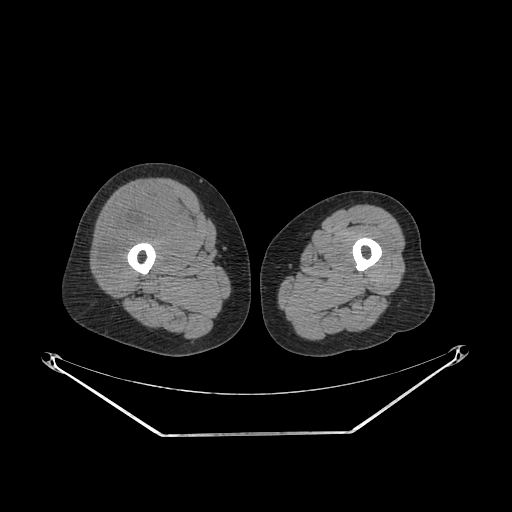
CT of an extremity soft-tissue mass (from a PET/CT study), one axial slice. Slice 237 of 311 in the series (ordered by position). Reconstruction kernel SOFT. 140 kVp. Soft-tissue window (W 400 / L 40 HU). 3.75 mm slice thickness. 512 × 512 image matrix, field of view 500 × 500 mm. Female patient. Case-level facts recorded for this patient, not image findings: histological type: pleiomorphic undifferentiated sarcoma; grade: high; site of the primary tumour: right quadricep.
Structures marked on this image (expert contour drawn on MRI and transferred to this co-registered scan by the dataset authors):
- tumour plus oedema (research contour): bounding box <100,194,184,280> (left, top, right, bottom; pixels)
- tumour (research contour): <100,194,184,280>